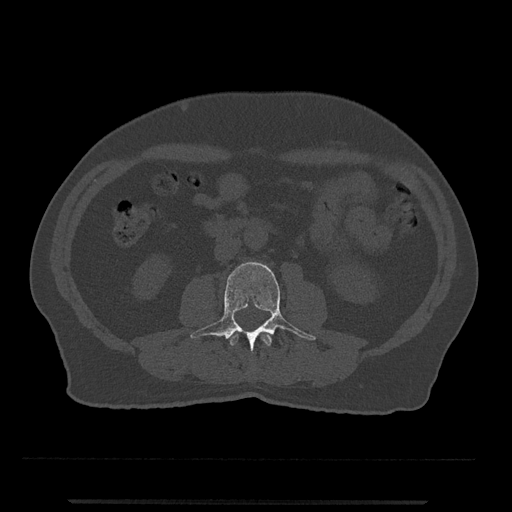
CT including the spine, one axial slice. Reconstruction kernel Br40s/3. 120 kVp. Bone window (W 1800 / L 400 HU). 0.5 mm slice thickness. 512 × 512 image matrix, field of view 419 × 419 mm. Male patient, age 63 years. Case-level facts recorded for this patient, not image findings: primary cancer: prostate.
Outlined on this slice (semi-automatically segmented with operator editing):
- L2 vertebra: box from (x=229, y=333) to (x=272, y=347) px
- L3 vertebra: (x=190, y=262)–(x=316, y=351)